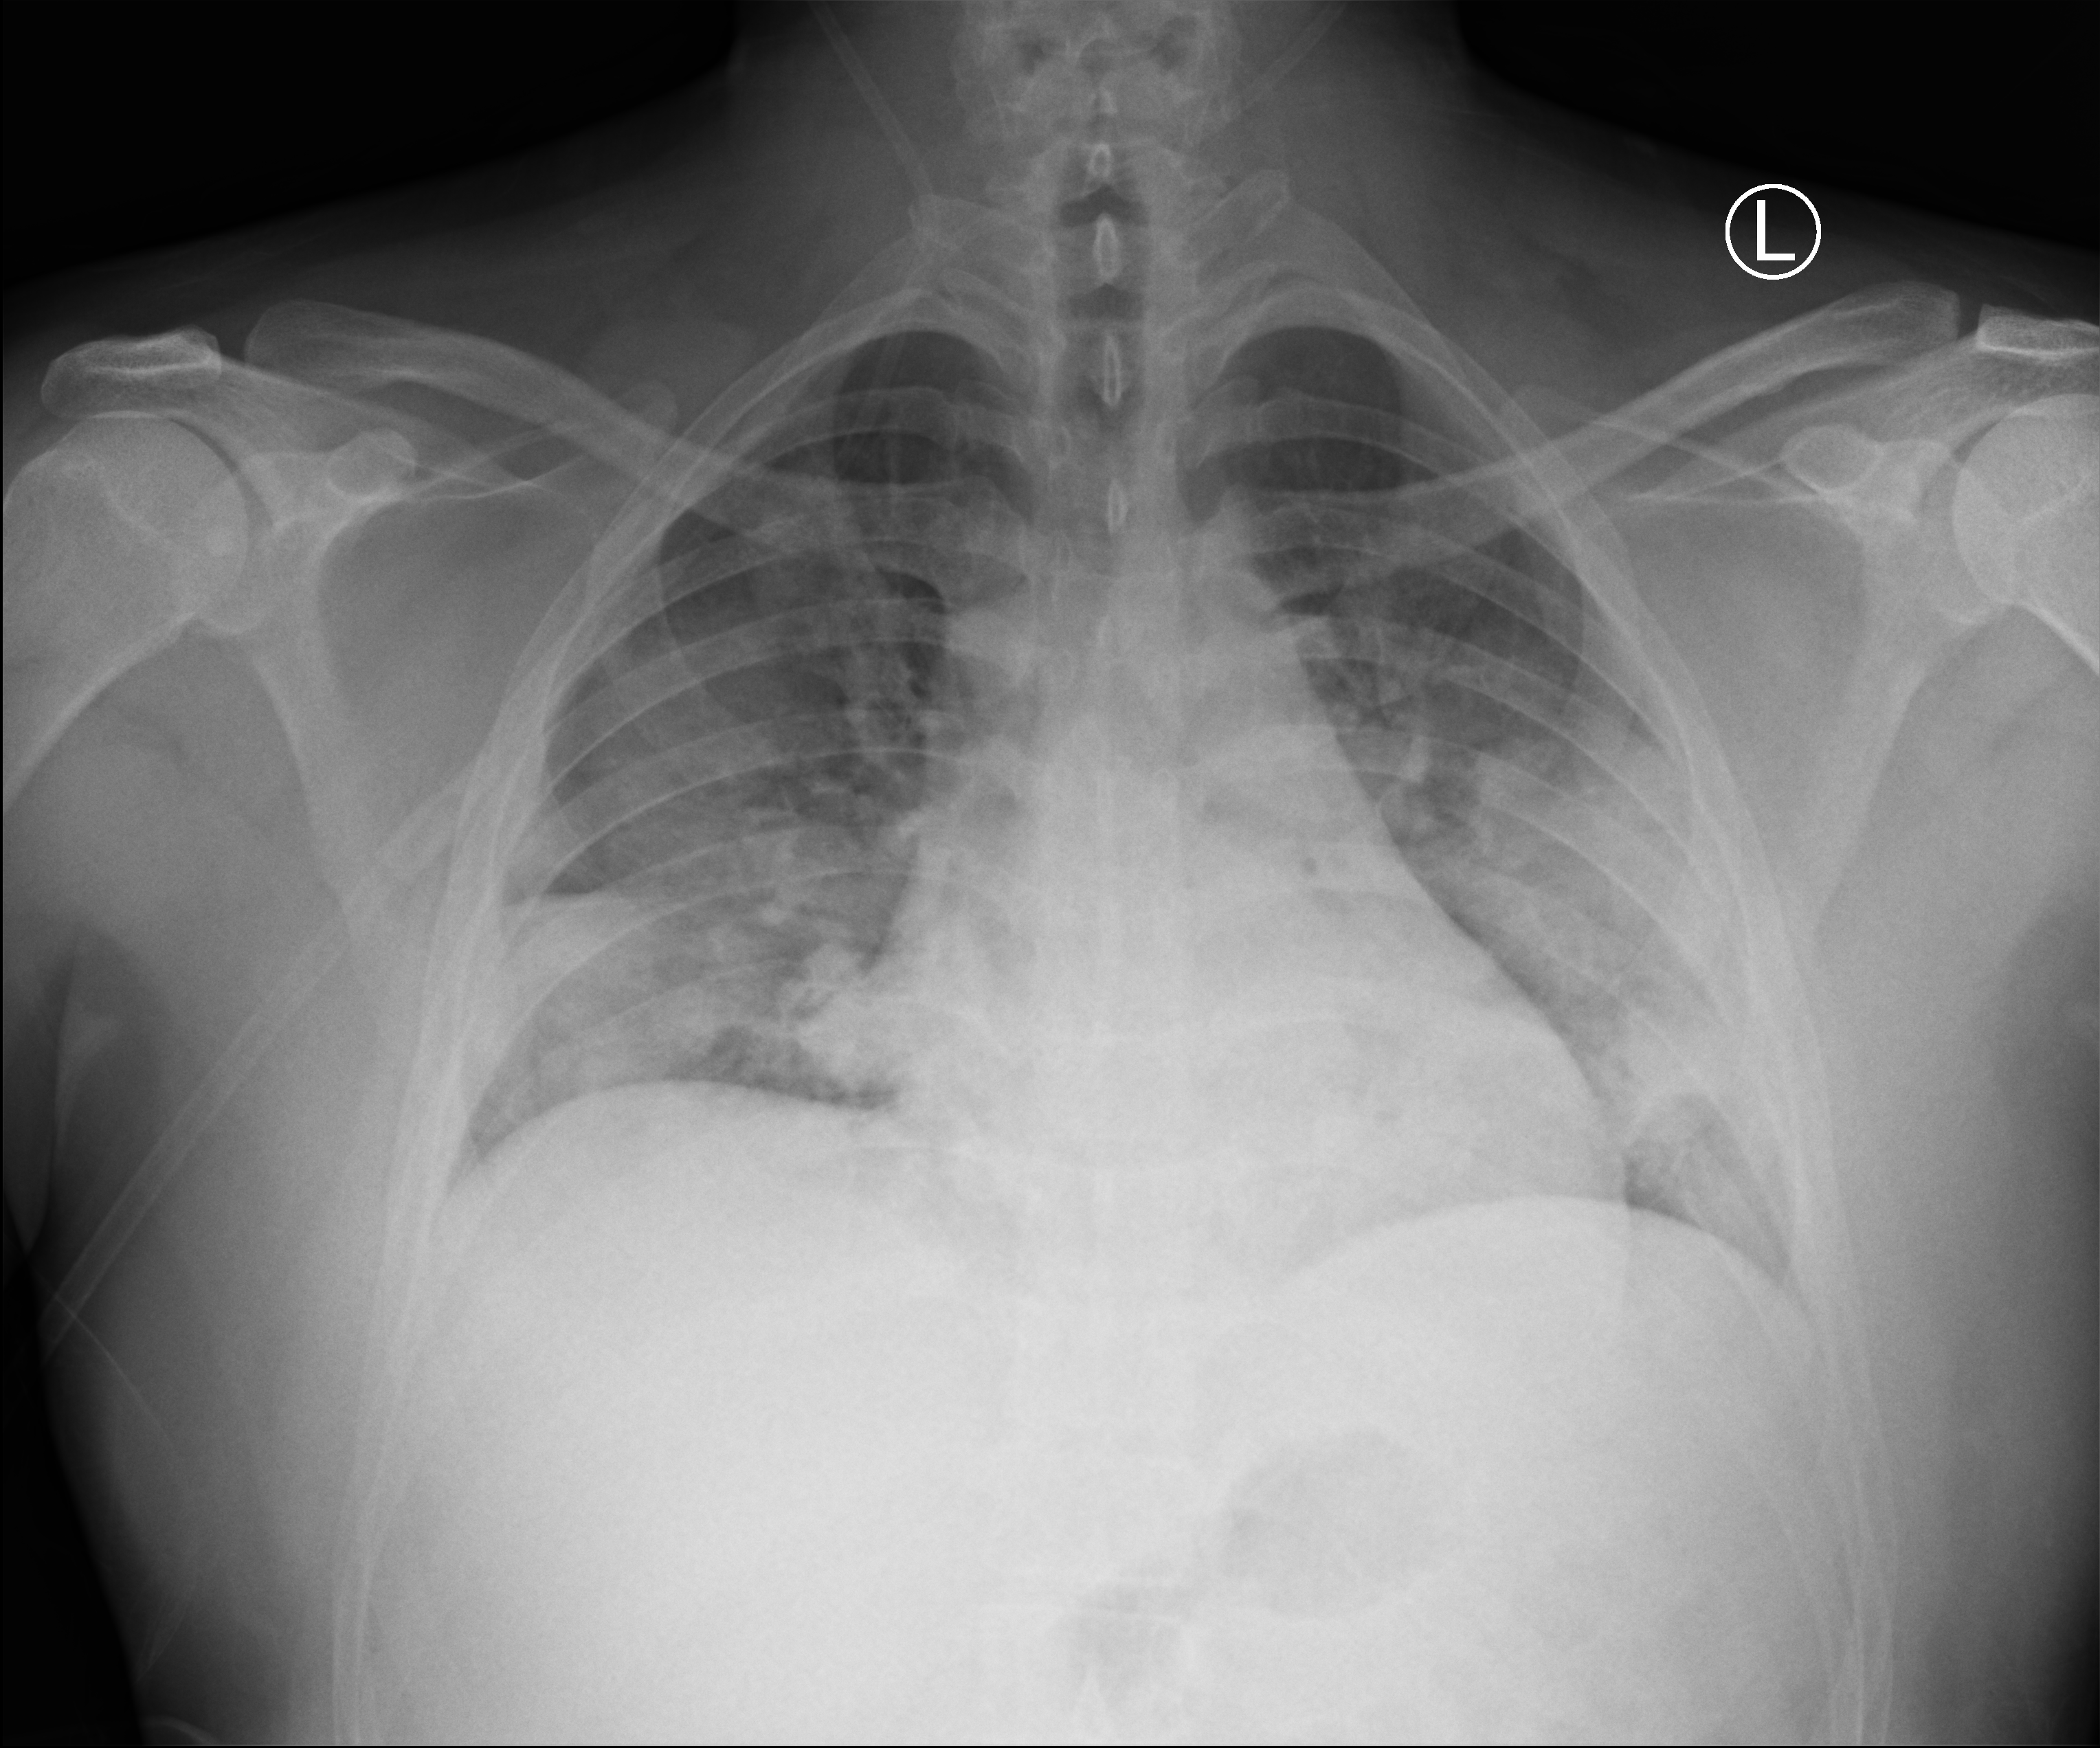
Chest X-ray (portable); anteroposterior (AP) projection. Male patient hospitalised with COVID-19, age 18–59 years.
Admission-level facts for this patient (not findings on this image; timing relative to this image not recorded):
- admitted to intensive care during this hospital stay: no
- mechanically ventilated during this hospital stay: no
- hypertension (admission record): no